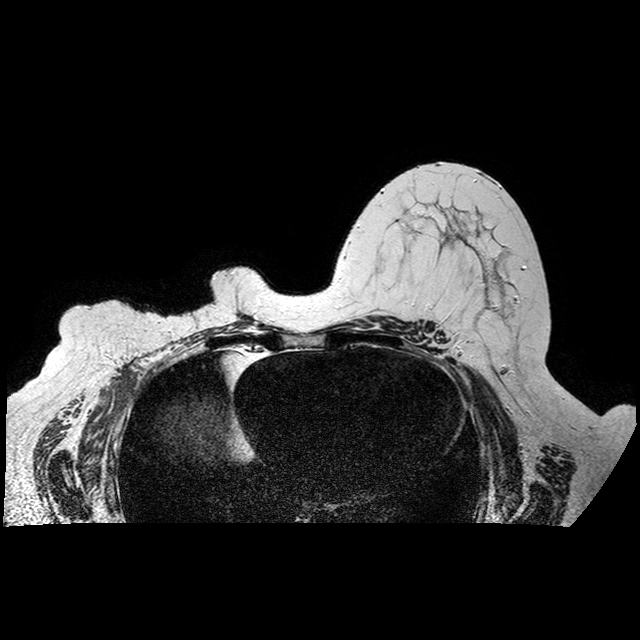
Breast MRI examination; 2 images, each one mid-volume slice chosen by position.
Image 1: fluid-sensitive (T2/STIR) axial slice, slice 47 of 92, 2 mm slice thickness.
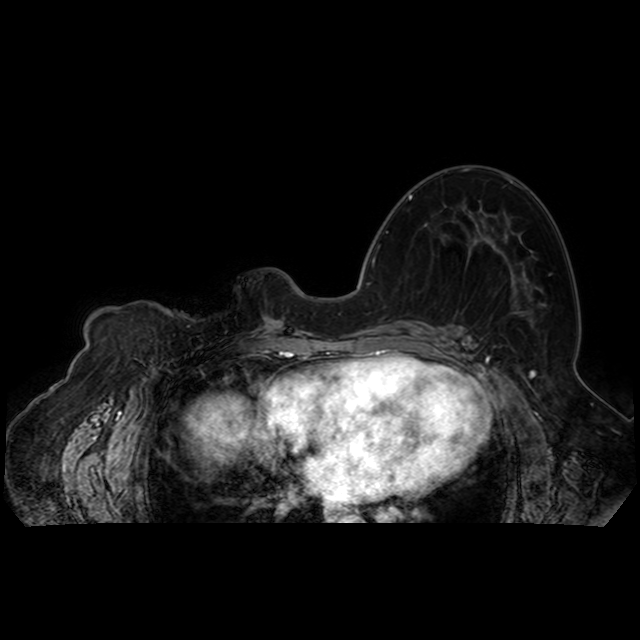
Image 2: axial dynamic contrast-enhanced T1-weighted image, series "AX BLISS_AUTO SENSE", slice 47 of 92, dynamic phase 5 of 8.
Patient-level pathology facts (from the clinical record, not from the images): pathology diagnosis: invasive intraductal CA (right breast); receptor status (as recorded): ER neg, PR pos, HER2 neg.